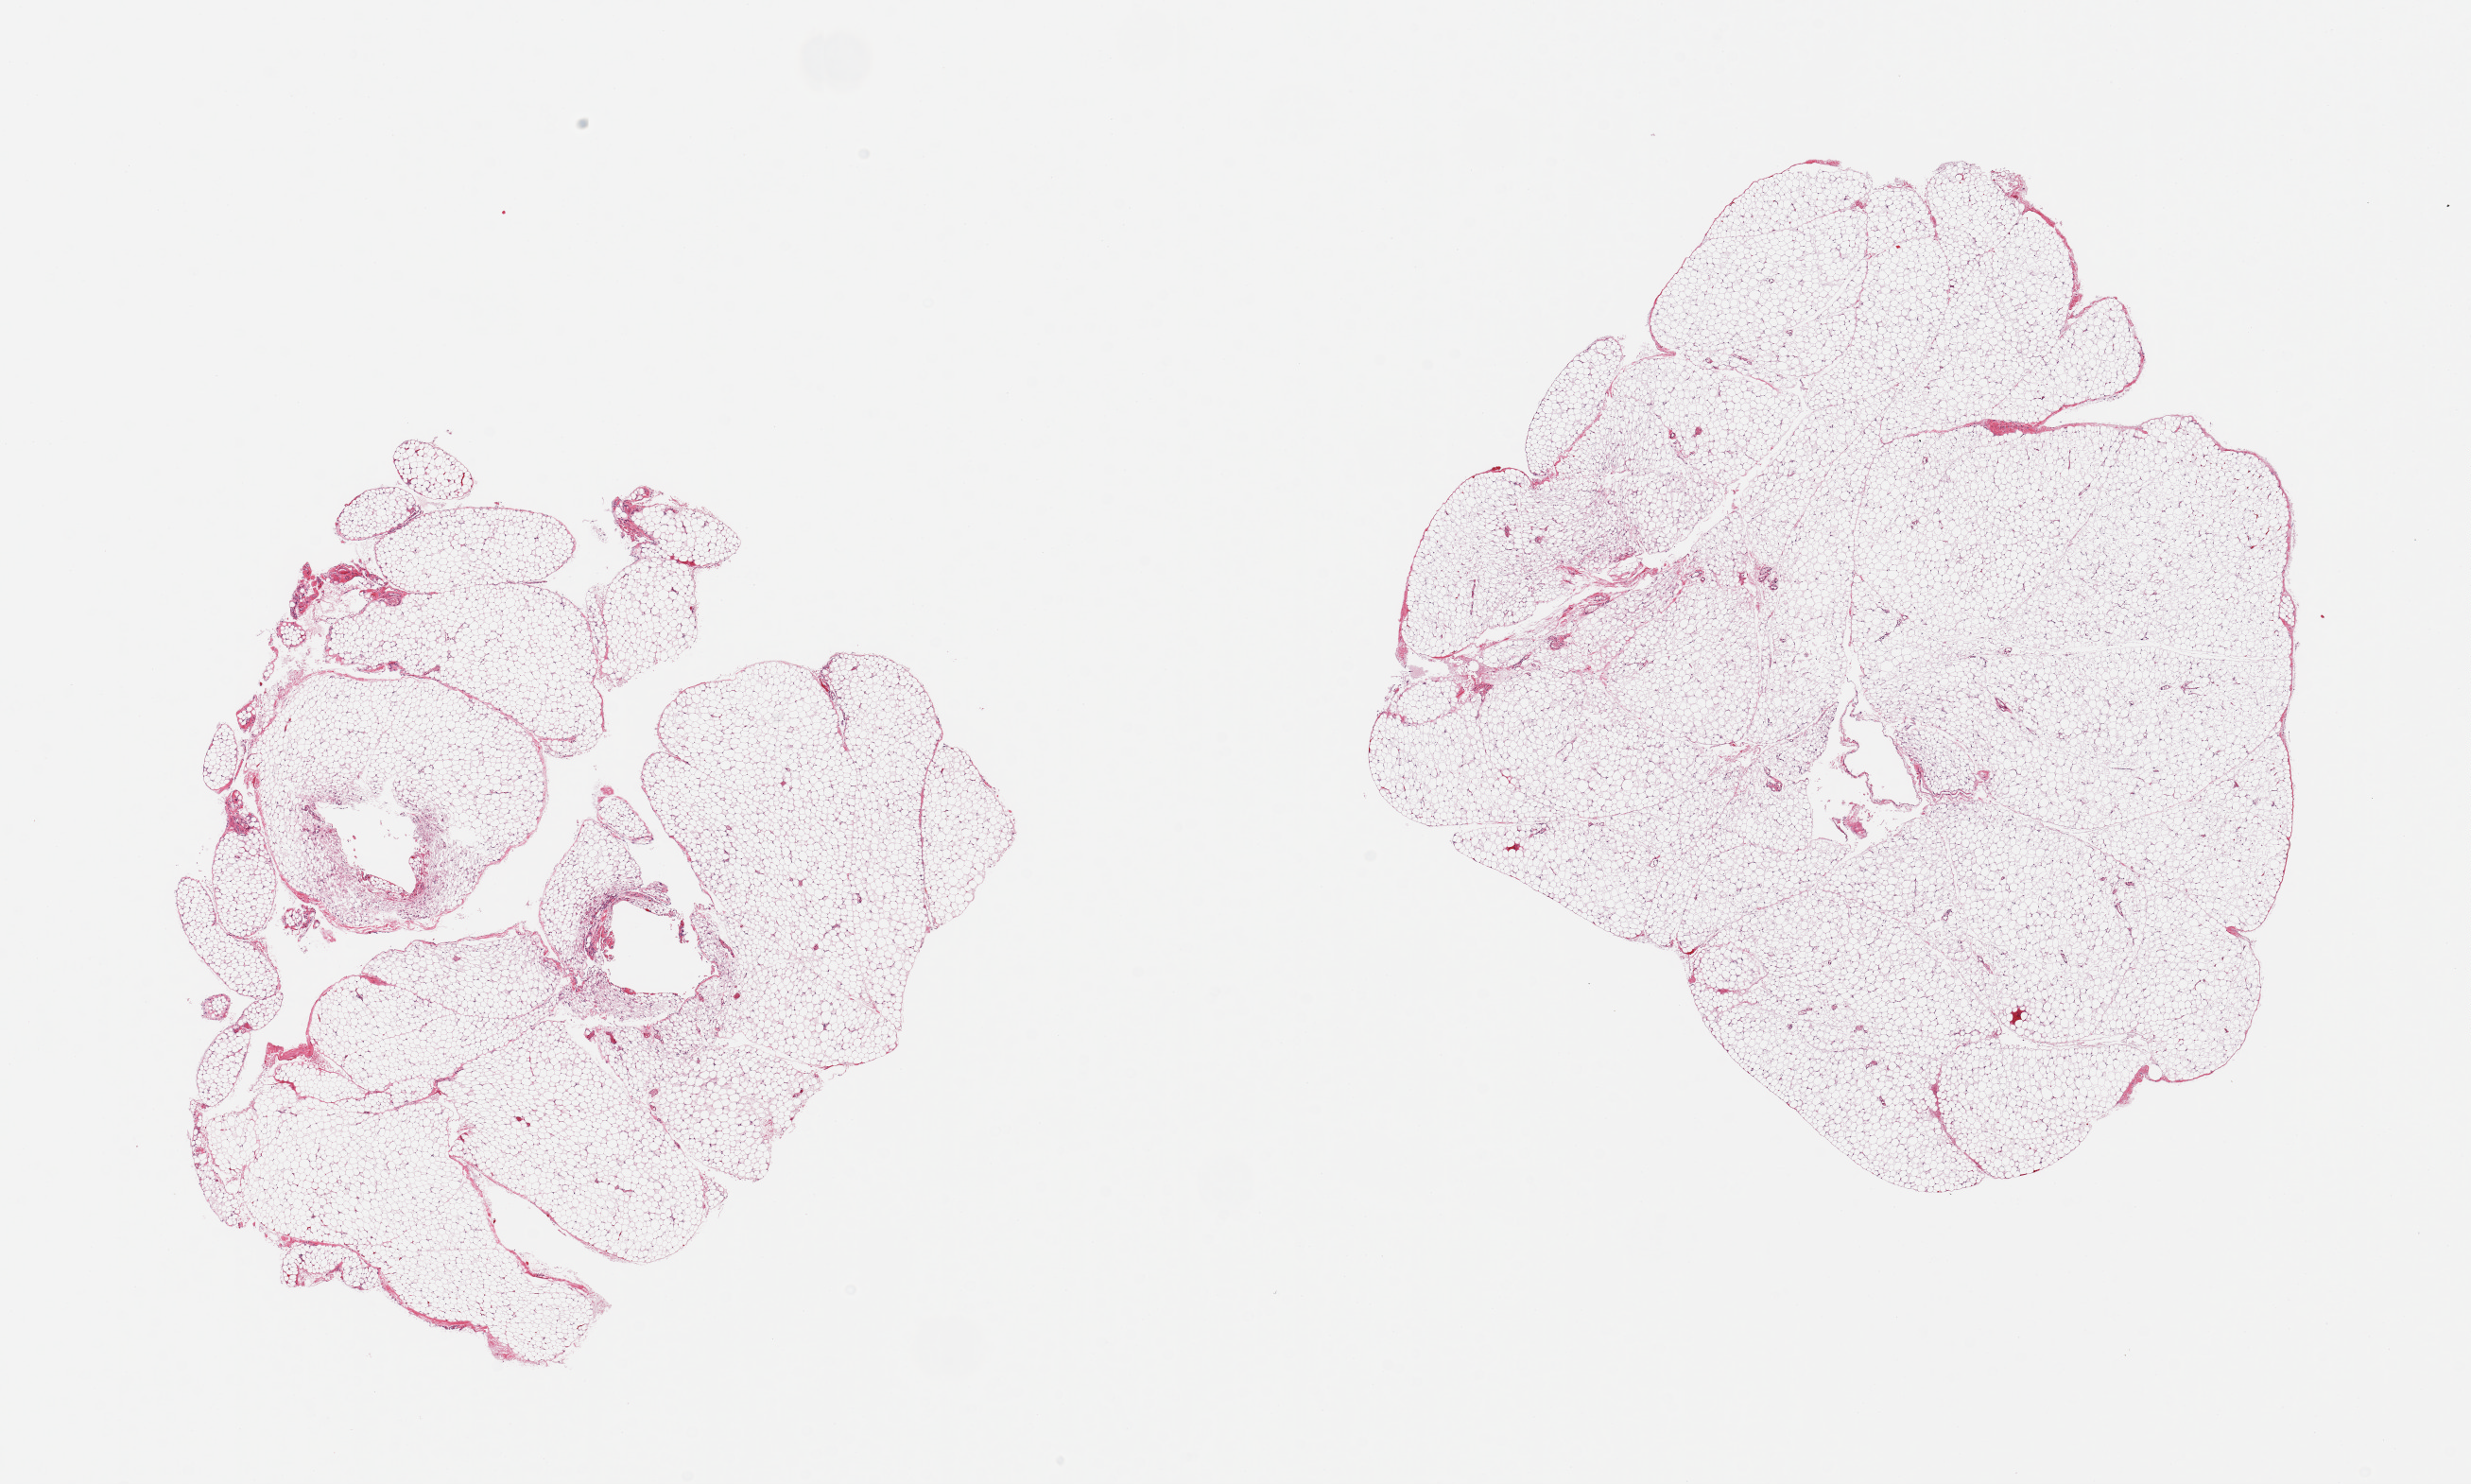
Digitized H&E-stained section, brightfield, whole scanned area (about 20.7 x 12.4 mm) shown as a low-resolution overview; PAXgene-fixed, paraffin-embedded tissue; section of omentum (target tissue); tissue donor sample. Male donor.
Review note (as recorded): 2 pieces; lobulated fat.